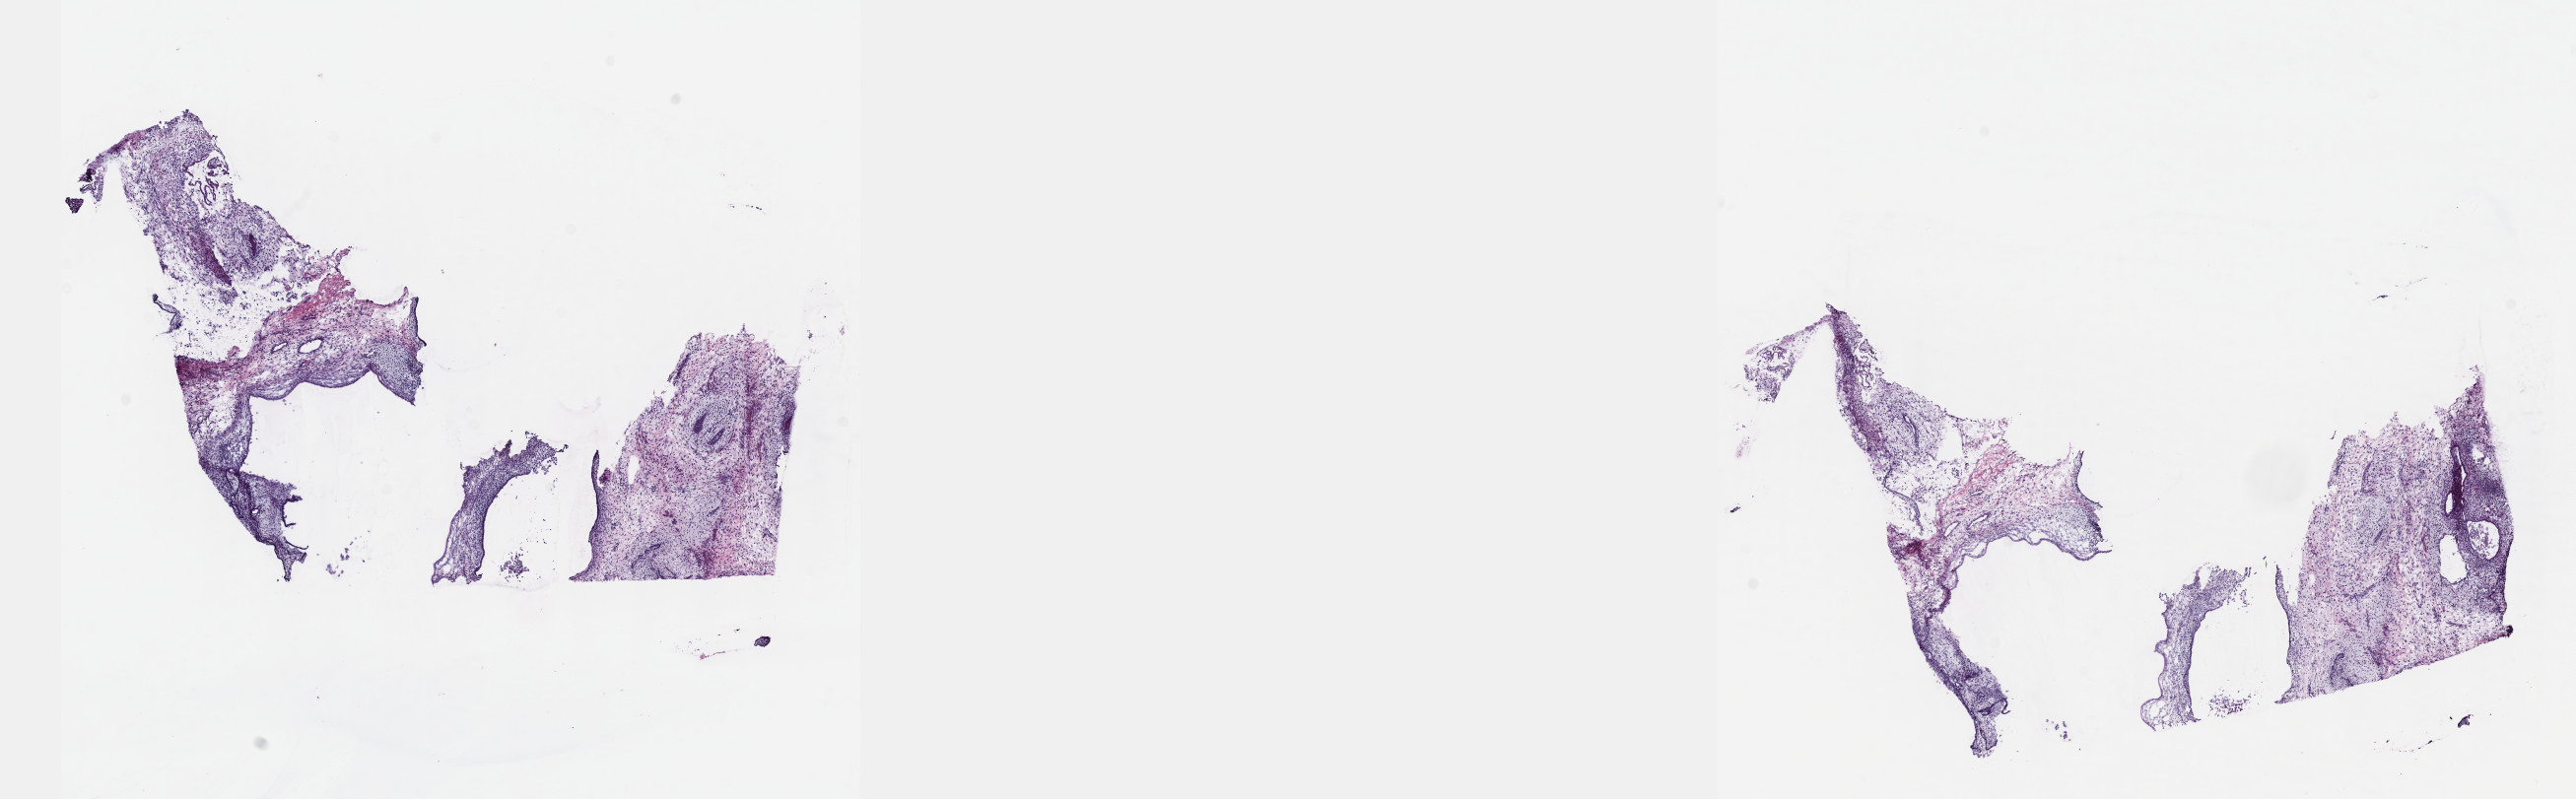
Hematoxylin and eosin (H&E) stained whole-slide image, a low-resolution overview of the entire scanned area, about 21.1 x 6.6 mm. Patient sex: male. Composition of this section per pathologist review: tumour cells 90%, tumour nuclei 95%, normal cells 0%, stromal cells 10%, necrosis 0%. Infiltration values recorded for this section: lymphocyte infiltration 0%, monocyte infiltration 0%, neutrophil infiltration 0%.
Specimen: frozen section; sample: primary tumour, testis.